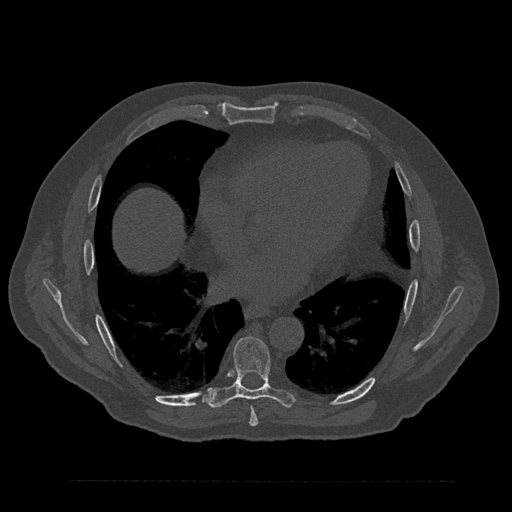
CT including the spine, one axial slice; position 462 of 797 along the scan axis; reconstruction kernel Br40s/3; bone window (W 1800 / L 400 HU); 512 × 512 image matrix, field of view 430 × 430 mm. Male patient, age 61 years. From the clinical record (not read from this slice): primary cancer: prostate.
Outlined on this slice (semi-automatically segmented with operator editing):
- T7 vertebra: bounding box [x1, y1, x2, y2] px = [249, 407, 258, 426]
- T8 vertebra: [208, 336, 295, 409]